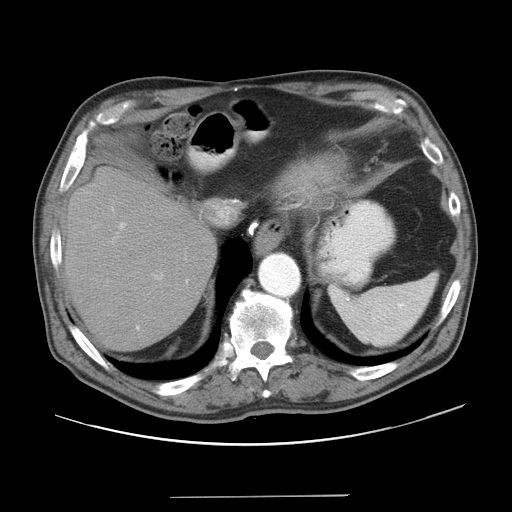
Contrast-enhanced abdominal CT, one axial slice; slice 33 of 41 in the series (ordered by position); reconstruction kernel STANDARD; 120 kVp; intravenous contrast given; soft-tissue window (W 400 / L 40 HU); 5 mm slice thickness; 512 × 512 image matrix. Male patient, age 75 years. Case-level facts recorded for this patient, not image findings: diagnosis: colorectal cancer liver metastases, imaged before liver resection; multiple liver metastases: no; largest metastasis: 5.2 cm; chemotherapy before resection: no.
Outlined on this slice (expert manual segmentation):
- hepatic veins: box from (x=213, y=202) to (x=233, y=223) px
- liver: (x=68, y=170)–(x=215, y=349)
- planned liver remnant (the part of the liver to remain after resection): (x=88, y=214)–(x=215, y=349)
- portal vein (with intrahepatic branches): (x=119, y=222)–(x=163, y=330)